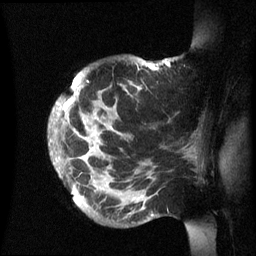
Breast MRI (dynamic contrast-enhanced), one sagittal slice; position 47 of 60 along the scan axis; dynamic contrast-enhanced series, image 2 of 3 at this slice position (ordered by acquisition); 1.5 T; TE 4.2 ms, TR 8.4 ms; 2.4 mm slice thickness; 256 × 256 image matrix, field of view 230 × 230 mm. Female patient, age 48 years.
Annotated regions visible in this slice (semi-automatically segmented with operator editing):
- analysis volume of interest (the breast-tissue region the enhancement analysis was run in; not a lesion): box from (x=49, y=57) to (x=202, y=236) px
- tumour enhancement mask (voxels above the 70 % enhancement threshold inside the analysis volume of interest): (x=63, y=61)–(x=167, y=152)